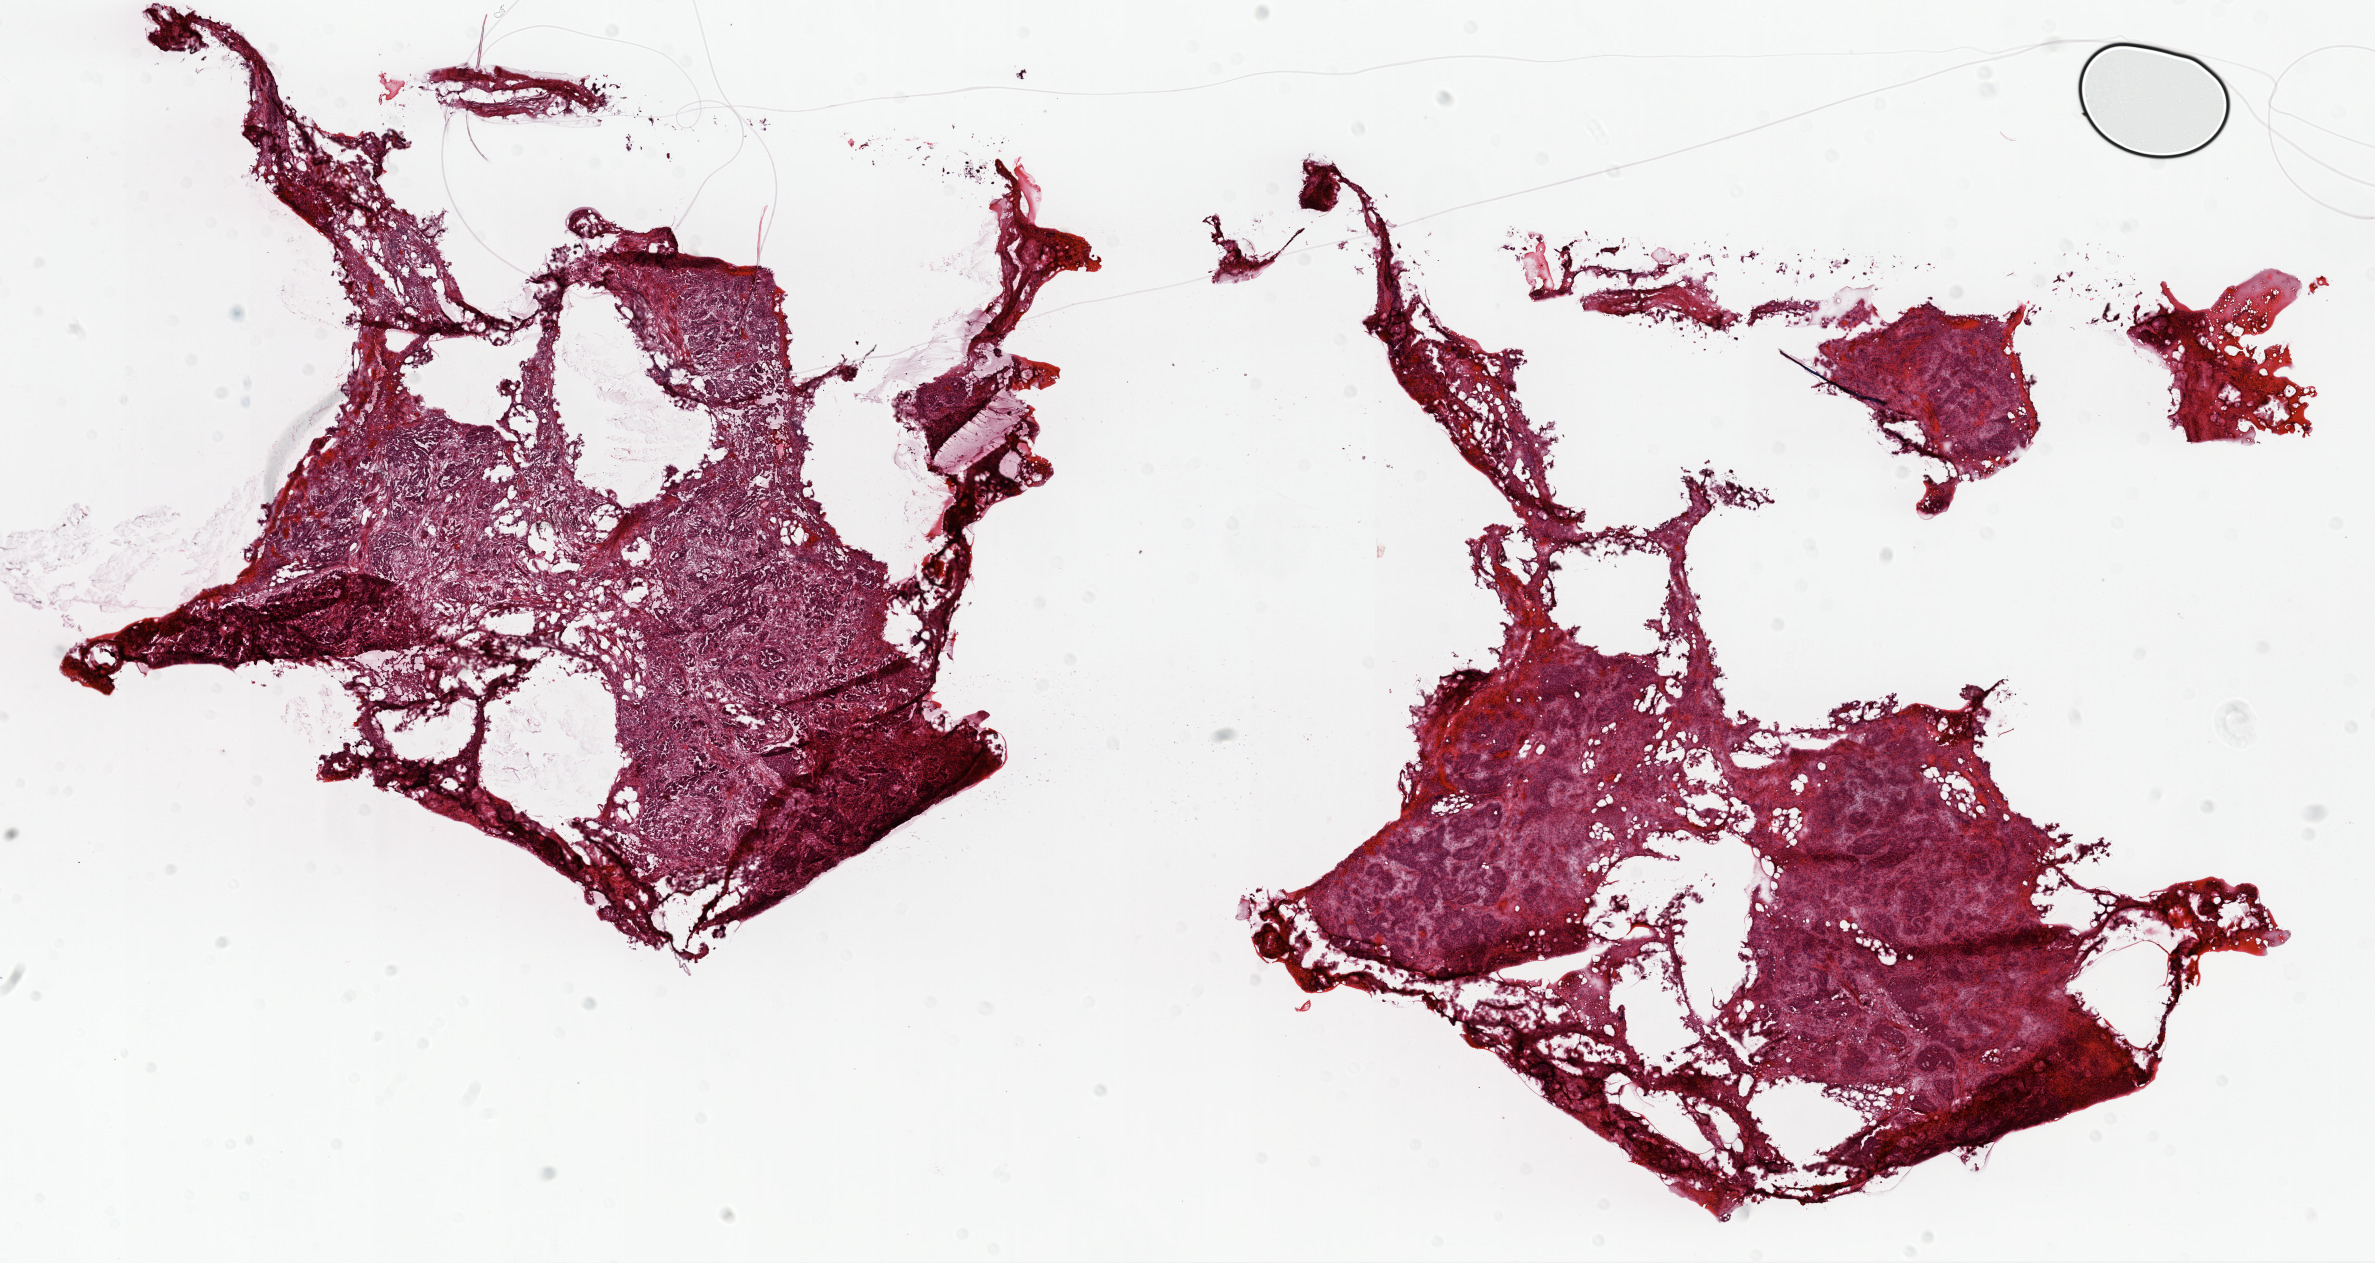
Digitized Hematoxylin and eosin (H&E) stained tissue section (whole slide), low-resolution overview of the scanned area, about 19.1 x 10.1 mm (acquisition: 20x scan). Frozen section. Ovary, primary tumour sample. Female patient; age at initial diagnosis 80 years. Histologic grade: G3 (poorly differentiated). Composition of this section per pathologist review: tumour cells 80%, tumour nuclei 80%, normal cells 0%, stromal cells 20%, necrosis 0%.
Pathologic diagnosis: Serous cystadenocarcinoma, NOS. FIGO stage: IIIC.